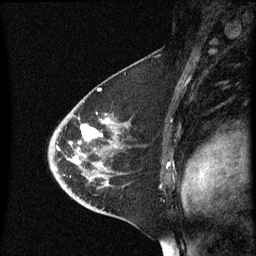
Breast MRI (dynamic contrast-enhanced), one sagittal slice; position 38 of 60 along the scan axis; dynamic contrast-enhanced series, image 2 of 3 at this slice position (ordered by acquisition); 1.5 T; TE 4.2 ms, TR 8.4 ms; 2.3 mm slice thickness; 256 × 256 image matrix. Female patient, age 46 years. Case-level facts recorded for this patient, not image findings: setting: breast cancer imaged before/during neoadjuvant chemotherapy; receptor status: HER2-positive.
Annotated regions visible in this slice (semi-automatic segmentation, software-assisted and operator-edited):
- analysis volume of interest (the breast-tissue region the enhancement analysis was run in; not a lesion): bounding box <49,96,130,187> (left, top, right, bottom; pixels)
- tumour enhancement mask (voxels above the 70 % enhancement threshold inside the analysis volume of interest): <73,126,99,161>